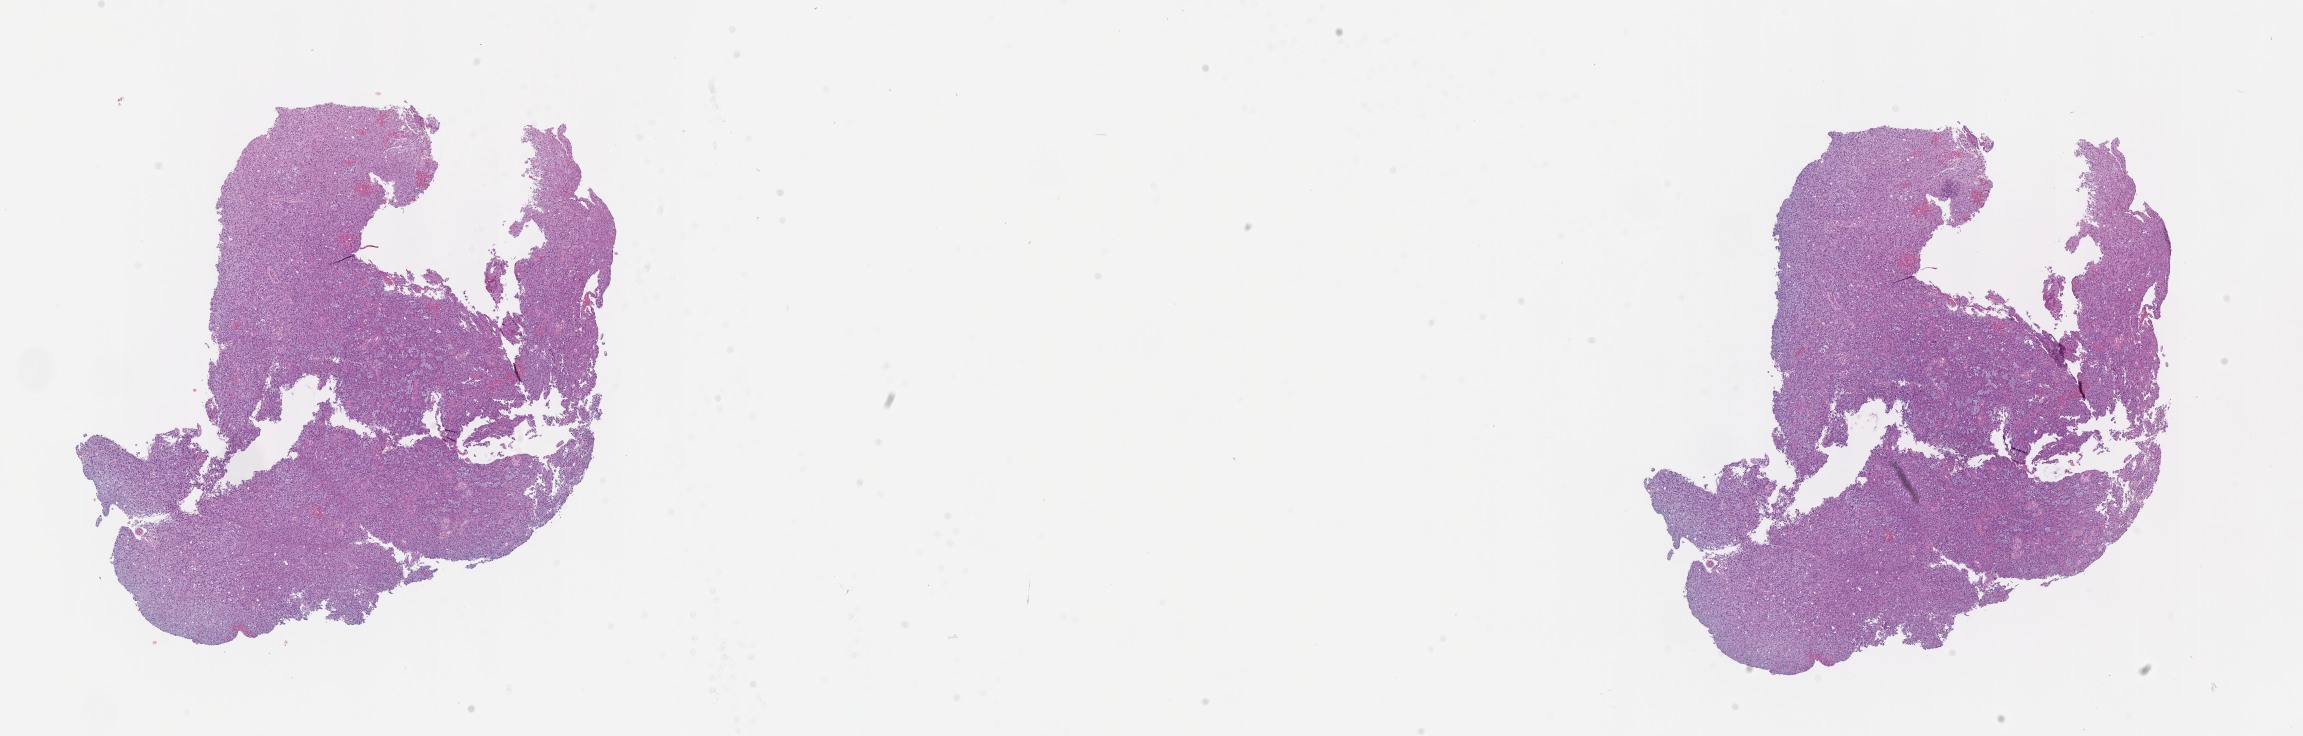
Whole-slide histology image, Hematoxylin and eosin (H&E) stained, low-resolution overview of the scanned area, about 18.6 x 5.9 mm (from a 40x scan). FFPE section. Sample: primary tumour, brain. Patient: female, age at initial diagnosis 33 years. Histologic grade: G3 (poorly differentiated).
• pathologic diagnosis: Astrocytoma, anaplastic
• laterality: right